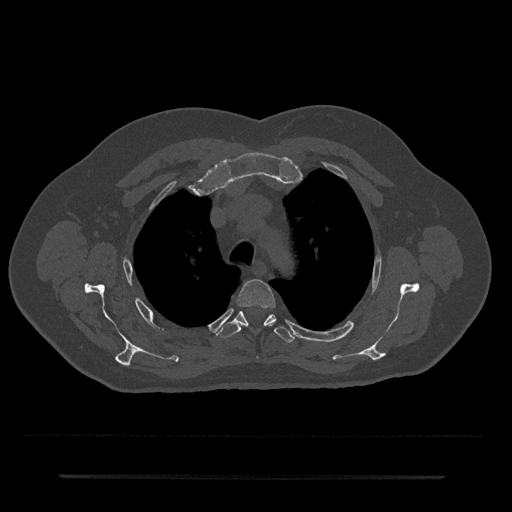
CT including the spine, one axial slice. Position 547 of 797 along the scan axis. Reconstruction kernel Br40s/3. 120 kVp. Bone window (W 1800 / L 400 HU). 0.5 mm slice thickness. 512 × 512 image matrix, field of view 437 × 437 mm. Male patient, age 69 years. Case-level facts recorded for this patient, not image findings: primary cancer: prostate.
Structures marked on this image (semi-automatically segmented with operator editing):
- T3 vertebra: box from (x=237, y=279) to (x=276, y=326) px
- T4 vertebra: (x=216, y=311)–(x=294, y=343)